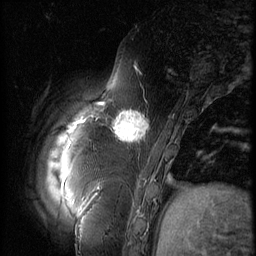
Breast MRI (dynamic contrast-enhanced), one sagittal slice. Slice 11 of 60 in the series (ordered by position). 3 images stored at this slice position (order not interpretable as contrast timing). 1.5 T. TE 4.2 ms, TR 9 ms. 256 × 256 image matrix. Patient: female, 57 years. From the clinical record (not read from this slice): setting: breast cancer imaged before/during neoadjuvant chemotherapy; receptor status: triple-negative.
Outlined on this slice (semi-automatic segmentation, software-assisted and operator-edited):
- analysis volume of interest (the breast-tissue region the enhancement analysis was run in; not a lesion): bounding box (x1, y1, x2, y2) in pixels: (106, 101, 157, 152)
- tumour enhancement mask (voxels above the 140 % enhancement threshold inside the analysis volume of interest): (111, 111, 149, 143)